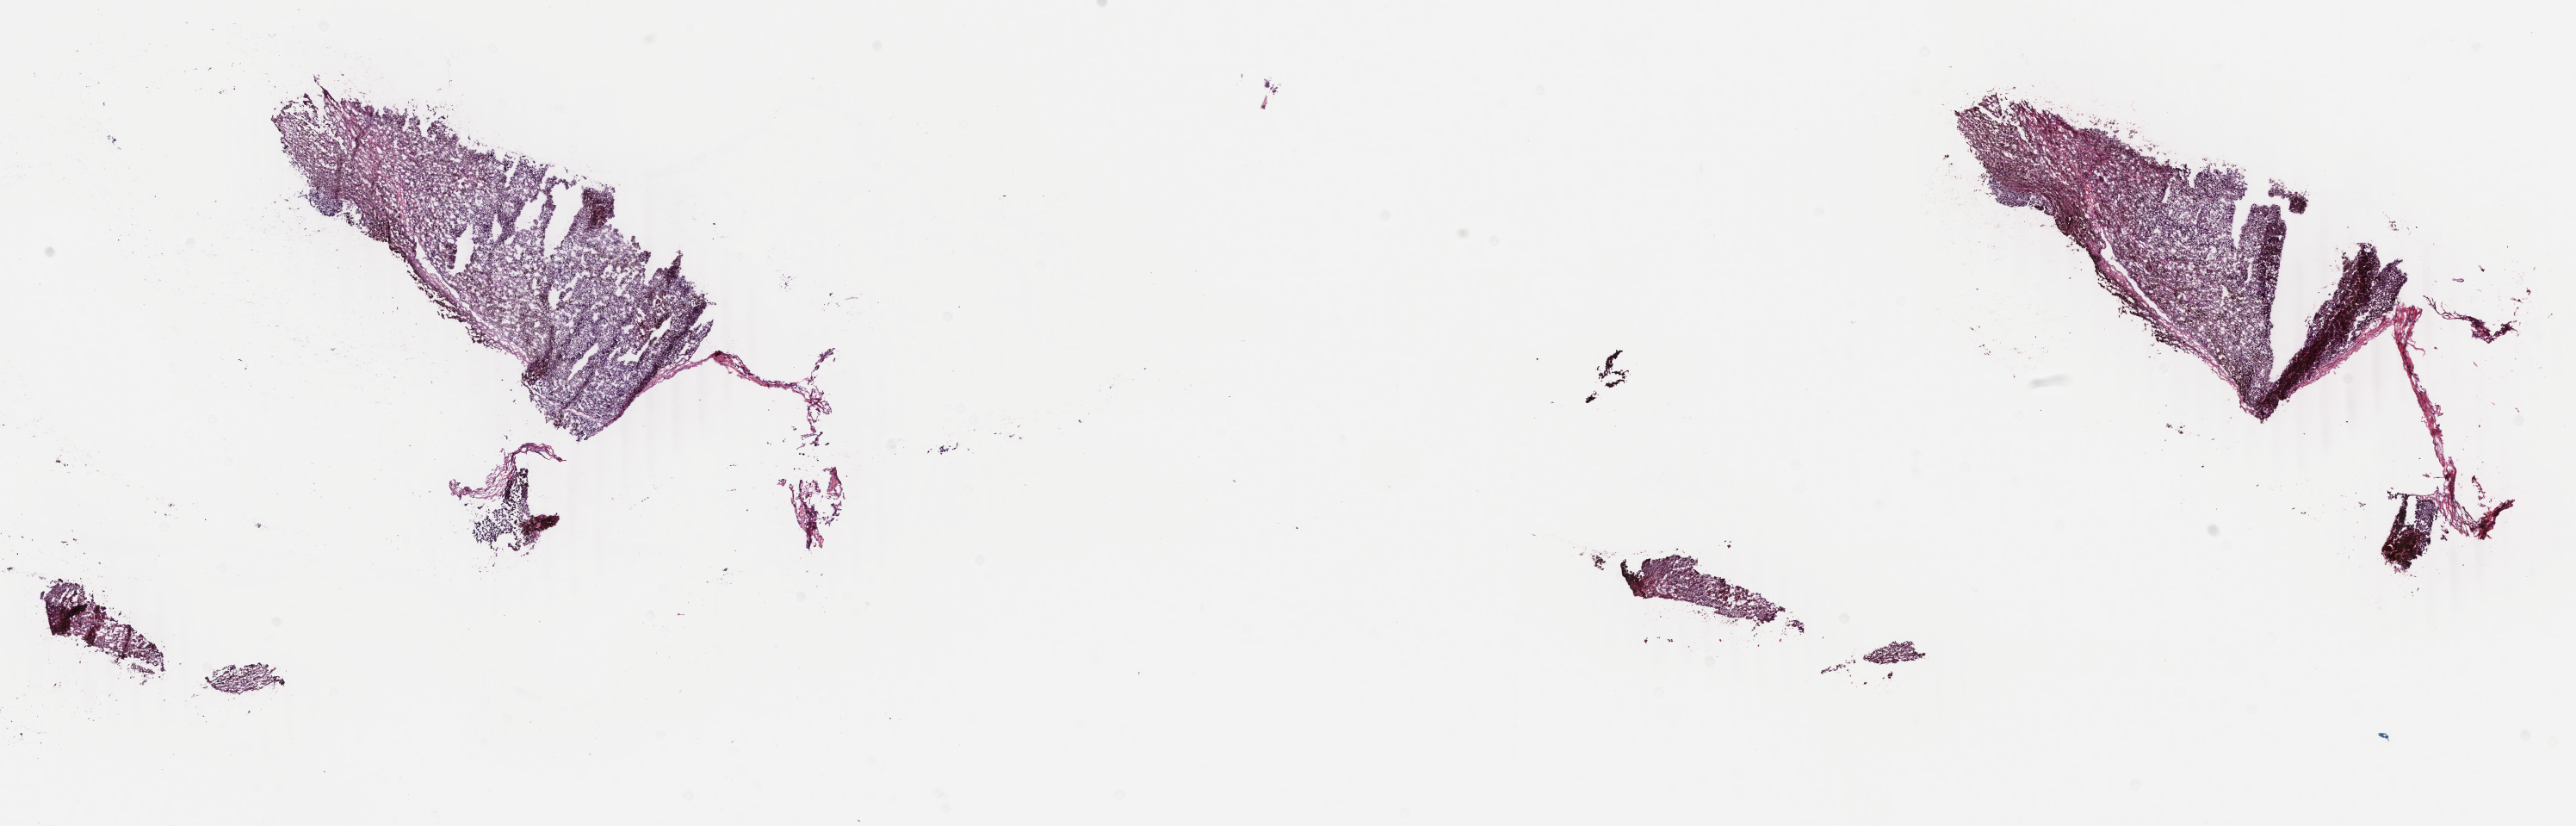
H&E whole-slide image — whole scanned area (about 23.8 x 7.6 mm) shown as a low-resolution overview, frozen section from the top of the tissue portion, metastatic tumour sample. Male patient; age at initial diagnosis 24 years. Slide review estimates, as recorded: tumour cells 85%, tumour nuclei 85%, normal cells 0%, stromal cells 15%, necrosis 0%. Infiltration values recorded for this section: lymphocyte infiltration 1%, monocyte infiltration 1%, neutrophil infiltration 1%.
This section: metastatic tumour tissue. Patient diagnosis: Malignant melanoma, NOS.